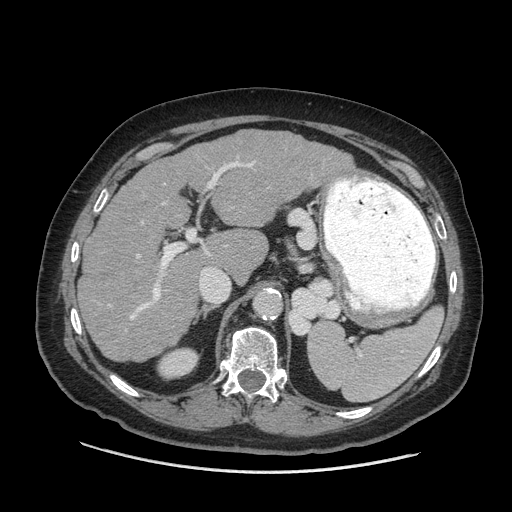
Contrast-enhanced abdominal CT (liver protocol), one axial slice. Slice 40 of 77 in the series (ordered by position). Reconstruction kernel STANDARD. 140 kVp. Soft-tissue window (W 400 / L 40 HU). 2.5 mm slice thickness. 512 × 512 image matrix, field of view 420 × 420 mm. From the clinical record (not read from this slice): diagnosis: hepatocellular carcinoma (patient treated with transarterial chemoembolisation; whether this scan precedes or follows treatment is not stated here); TNM stage (as recorded): Stage-I; Child-Pugh class: A; tumour differentiation: well differentiated; tumour nodularity: uninodular.
Outlined on this slice (semi-automatically segmented with operator editing):
- liver parenchyma outside the tumour (the mass and vessels are separate outlines, so this box may not span the whole liver): bounding box [x1, y1, x2, y2] px = [78, 130, 354, 362]
- liver vessels: [130, 161, 255, 320]